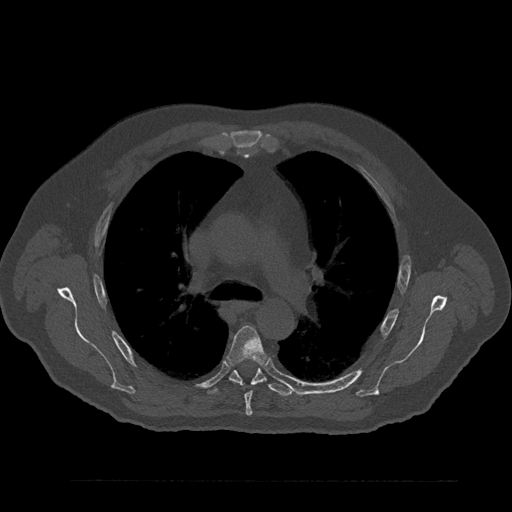
CT including the spine, one axial slice; slice 583 of 797 in the series (ordered by position); 120 kVp; bone window (W 1800 / L 400 HU); 0.5 mm slice thickness; 512 × 512 image matrix, field of view 430 × 430 mm. Patient: male, 61 years. From the clinical record (not read from this slice): primary cancer: prostate.
Outlined on this slice (semi-automatic segmentation, software-assisted and operator-edited):
- T5 vertebra: bounding box [x1, y1, x2, y2] px = [228, 326, 266, 416]
- T6 vertebra: [208, 364, 293, 396]